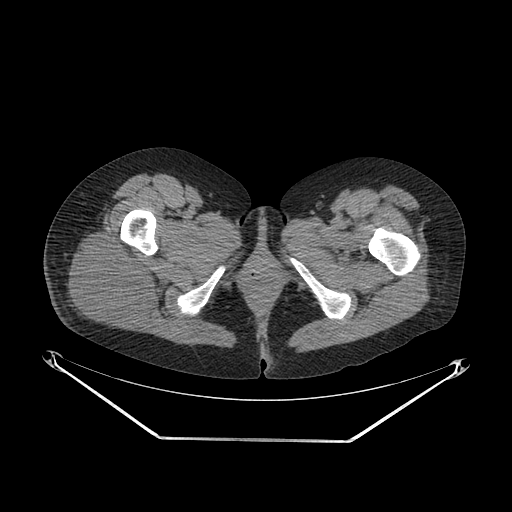
CT of an extremity soft-tissue mass (from a PET/CT study), one axial slice; reconstruction kernel SOFT; 140 kVp; soft-tissue window (W 400 / L 40 HU); 3.75 mm slice thickness; 512 × 512 image matrix, field of view 500 × 500 mm. Female patient. From the clinical record (not read from this slice): histological type: epithelioid sarcoma with vascular differentiation; site of the primary tumour: right buttock.
Annotated regions visible in this slice (expert contour drawn on MRI and transferred to this co-registered scan by the dataset authors):
- gross tumour volume (mass): bounding box <66,235,152,327> (left, top, right, bottom; pixels)